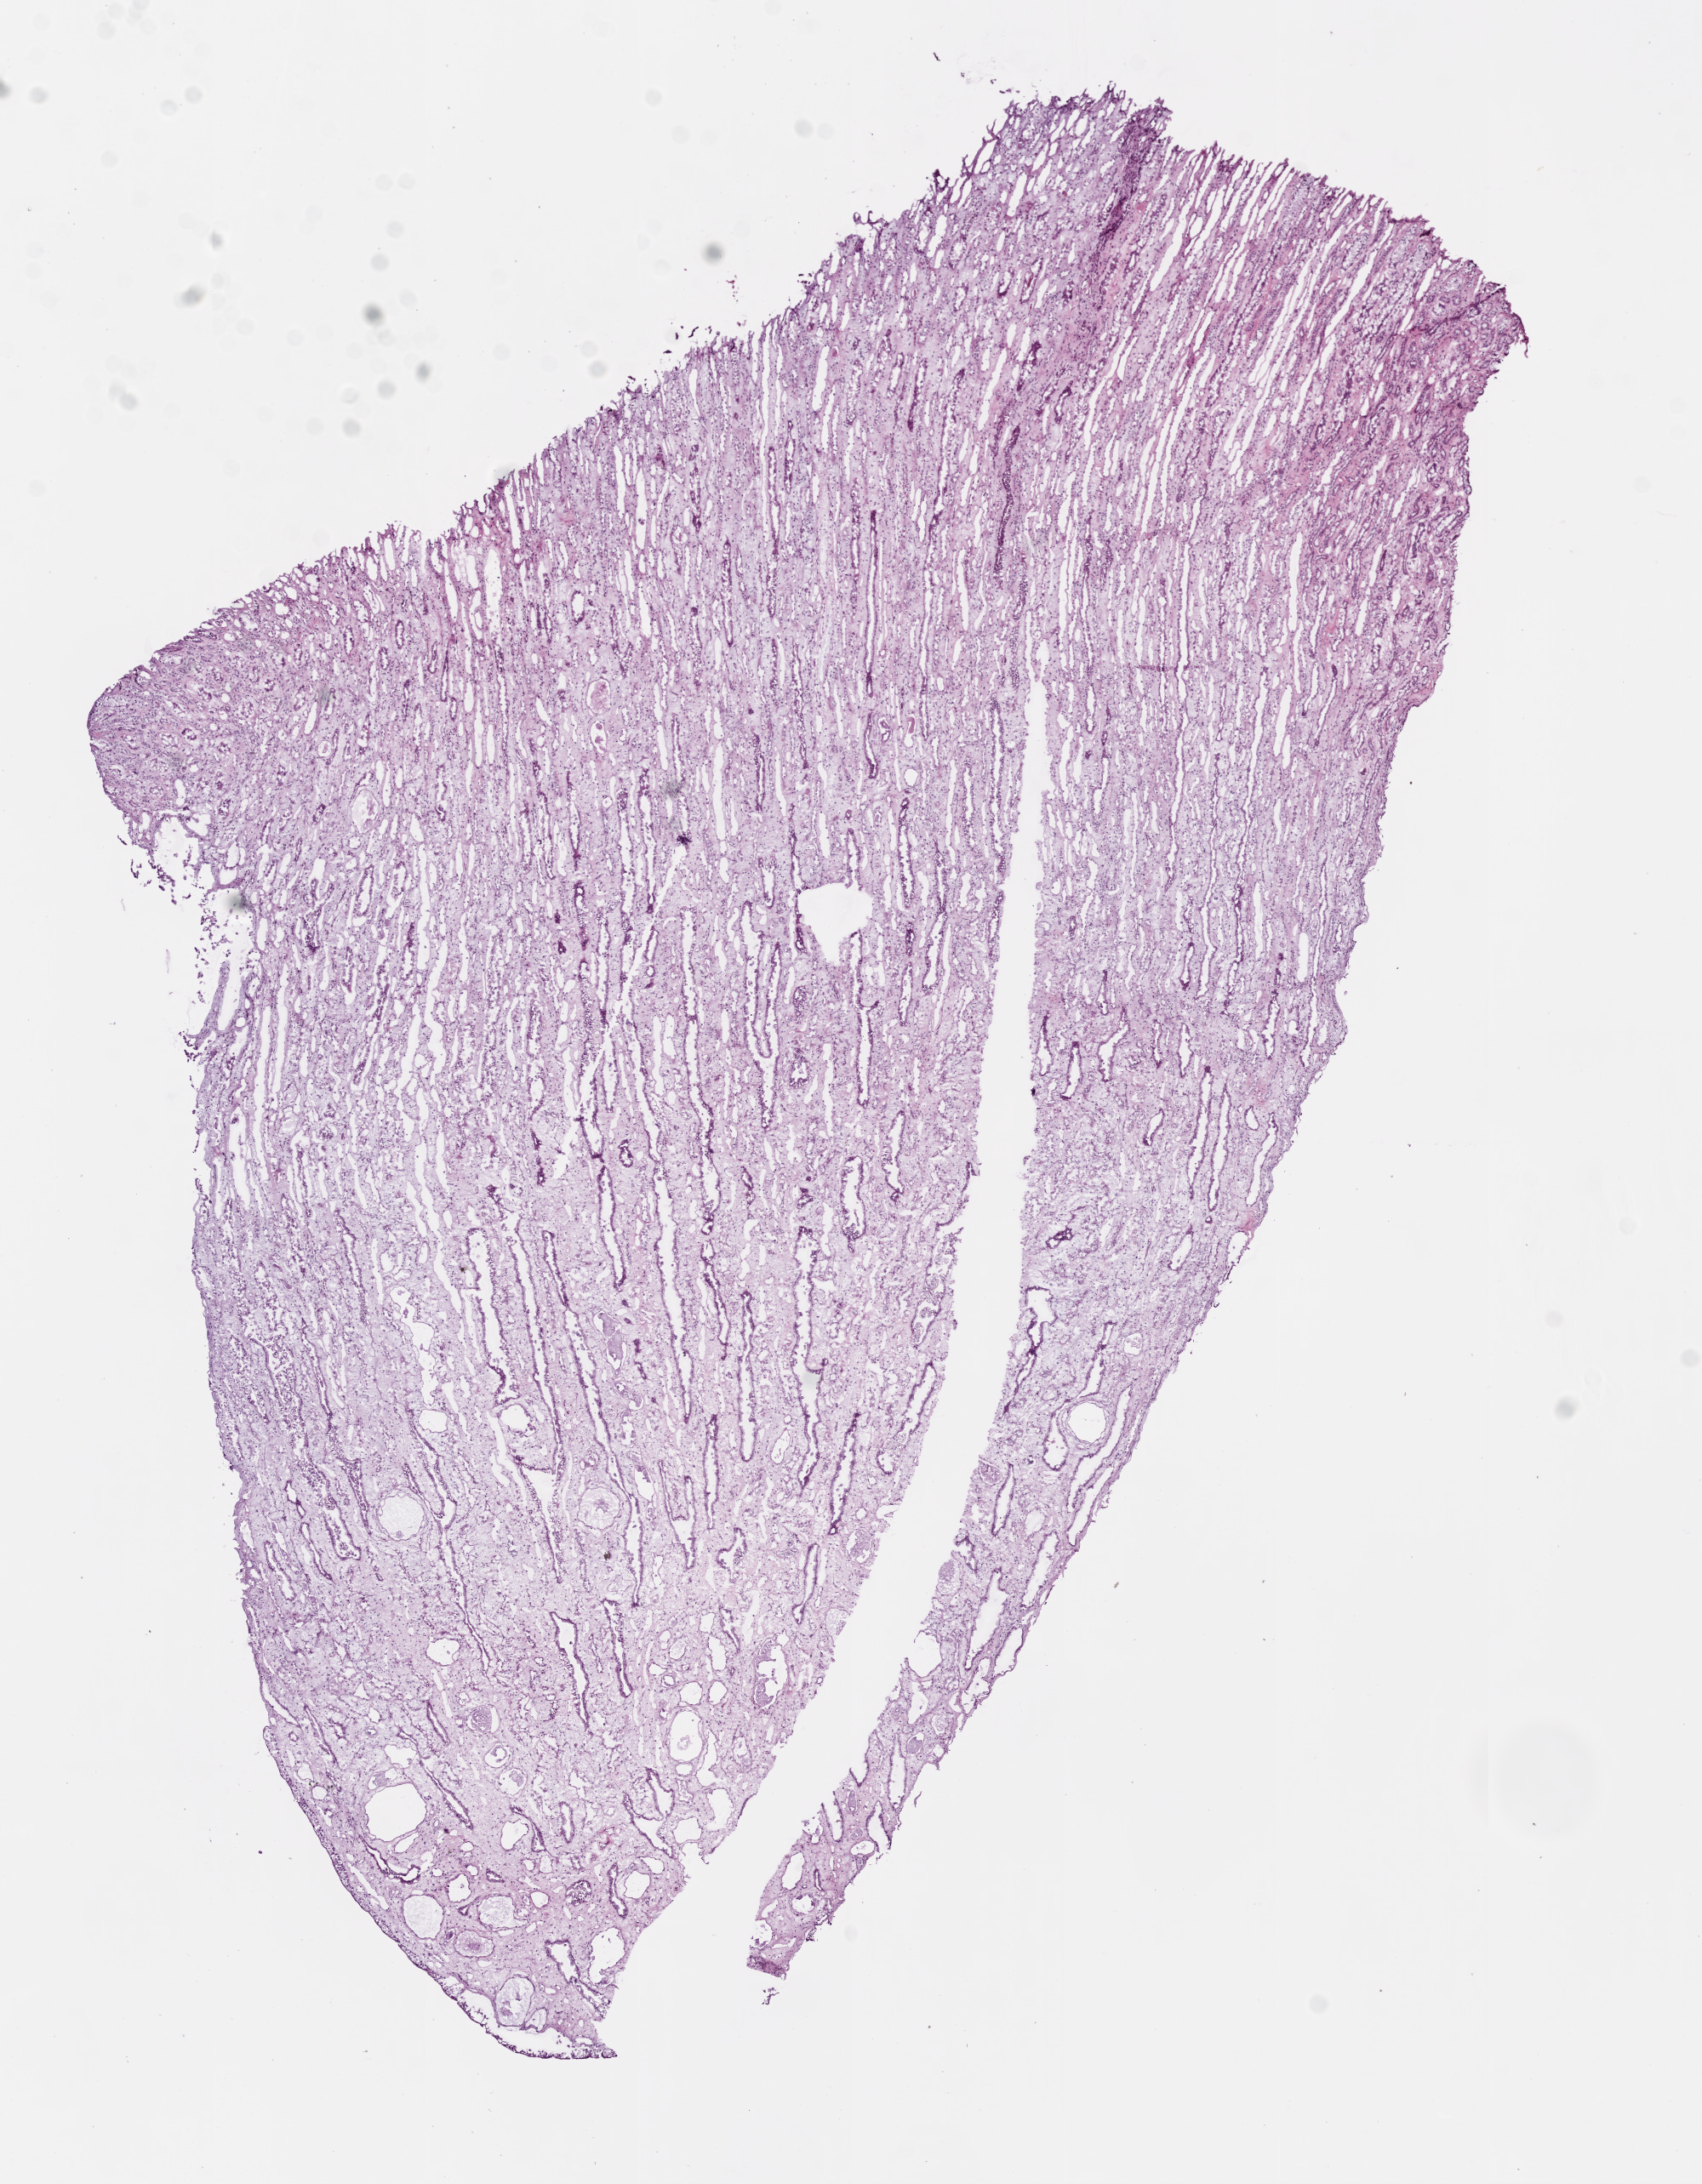
Whole-slide histology image, Hematoxylin and eosin (H&E) stained — whole scanned area (about 8.0 x 10.3 mm) shown as a low-resolution overview, frozen section from the bottom of the tissue portion, kidney, solid tissue normal (non-tumour tissue) sample. Patient: female, age at initial diagnosis 51 years.
This section: solid tissue normal (non-tumour) sample from the same patient. Patient diagnosis: Clear cell adenocarcinoma, NOS.